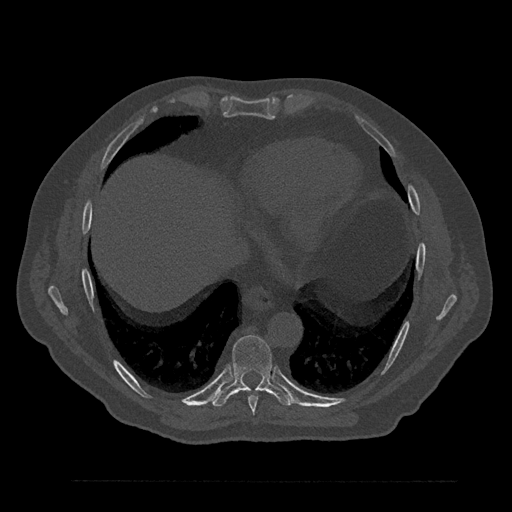
CT including the spine, one axial slice; position 423 of 797 along the scan axis; bone window (W 1800 / L 400 HU); 0.5 mm slice thickness; 512 × 512 image matrix, field of view 430 × 430 mm. Patient: male, 61 years. From the clinical record (not read from this slice): primary cancer: prostate.
Outlined on this slice (semi-automatic segmentation, software-assisted and operator-edited):
- T8 vertebra: box from (x=240, y=390) to (x=258, y=415) px
- T9 vertebra: (x=212, y=335)–(x=293, y=407)